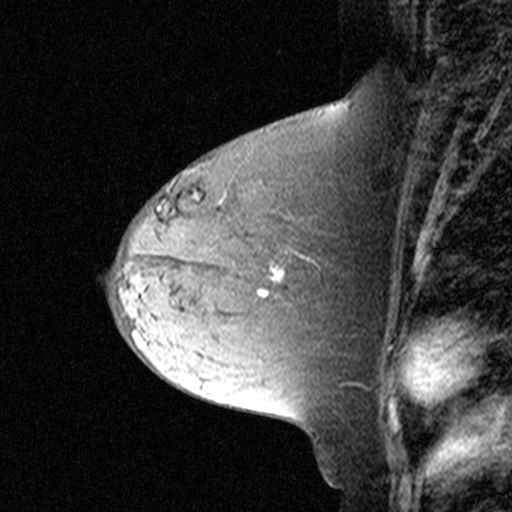
Breast MRI (dynamic contrast-enhanced), one sagittal slice; position 16 of 44 along the scan axis; dynamic contrast-enhanced study with each time point stored as its own series, time point 2 of 3 at this slice position (early post-contrast, ordered by acquisition time); 1.5 T; TE 4.5 ms, TR 11 ms; 512 × 512 image matrix, field of view 200 × 200 mm. Patient: female, 44 years. From the clinical record (not read from this slice): setting: breast cancer imaged before/during neoadjuvant chemotherapy; receptor status: triple-negative.
Structures marked on this image (semi-automatic segmentation, software-assisted and operator-edited):
- analysis volume of interest (the breast-tissue region the enhancement analysis was run in; not a lesion): bounding box [x1, y1, x2, y2] px = [174, 204, 303, 305]
- tumour enhancement mask (voxels above the 90 % enhancement threshold inside the analysis volume of interest): [260, 266, 285, 296]